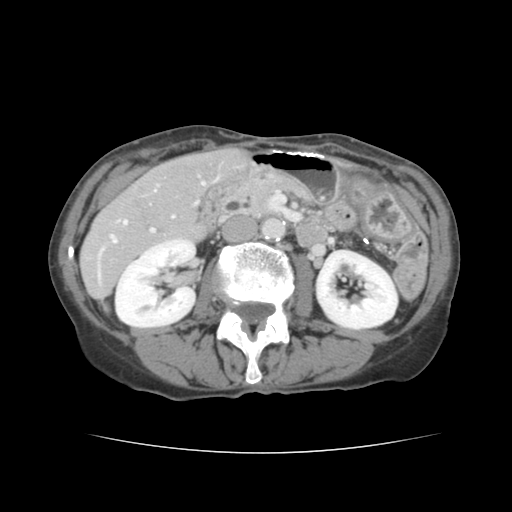
Contrast-enhanced abdominal CT, one axial slice; slice 55 of 136 in the series (ordered by position); 120 kVp; soft-tissue window (W 400 / L 40 HU); 2.5 mm slice thickness; 512 × 512 image matrix. Female patient, age 77 years. From the clinical record (not read from this slice): diagnosis: colorectal cancer liver metastases, imaged before liver resection; multiple liver metastases: yes; largest metastasis: 3 cm; chemotherapy before resection: yes.
Structures marked on this image (outlined manually by an expert reader):
- hepatic veins: bounding box <111,182,205,243> (left, top, right, bottom; pixels)
- liver: <81,148,245,301>
- planned liver remnant (the part of the liver to remain after resection): <167,149,246,195>
- portal vein (with intrahepatic branches): <98,229,155,278>